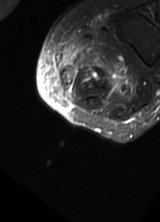
MRI of an extremity soft-tissue mass, one axial slice; position 5 of 69 along the scan axis; T2-weighted fat-saturated; MR volume resampled by the dataset authors to the PET/CT grid (not the native acquisition matrix); 3.27 mm slice thickness; 160 × 222 image matrix, field of view 156 × 217 mm. Female patient. From the clinical record (not read from this slice): histological type: pleomorphic leiomyosarcoma; grade: high; site of the primary tumour: left thigh.
Annotated regions visible in this slice (expert contour drawn on MRI and transferred to this co-registered scan by the dataset authors):
- gross tumour volume including surrounding oedema: box from (x=57, y=31) to (x=135, y=101) px